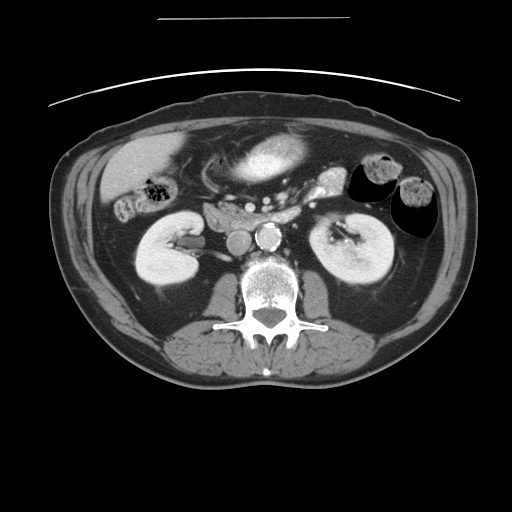
Contrast-enhanced abdominal CT, one axial slice; slice 14 of 49 in the series (ordered by position); 120 kVp; intravenous contrast given; soft-tissue window (W 400 / L 40 HU); 5 mm slice thickness; 512 × 512 image matrix. Male patient, age 57 years. Case-level facts recorded for this patient, not image findings: diagnosis: colorectal cancer liver metastases, imaged before liver resection; multiple liver metastases: yes; largest metastasis: 4 cm; disease in both lobes: no.
Annotated regions visible in this slice (outlined manually by an expert reader):
- liver: bounding box <100,133,182,200> (left, top, right, bottom; pixels)